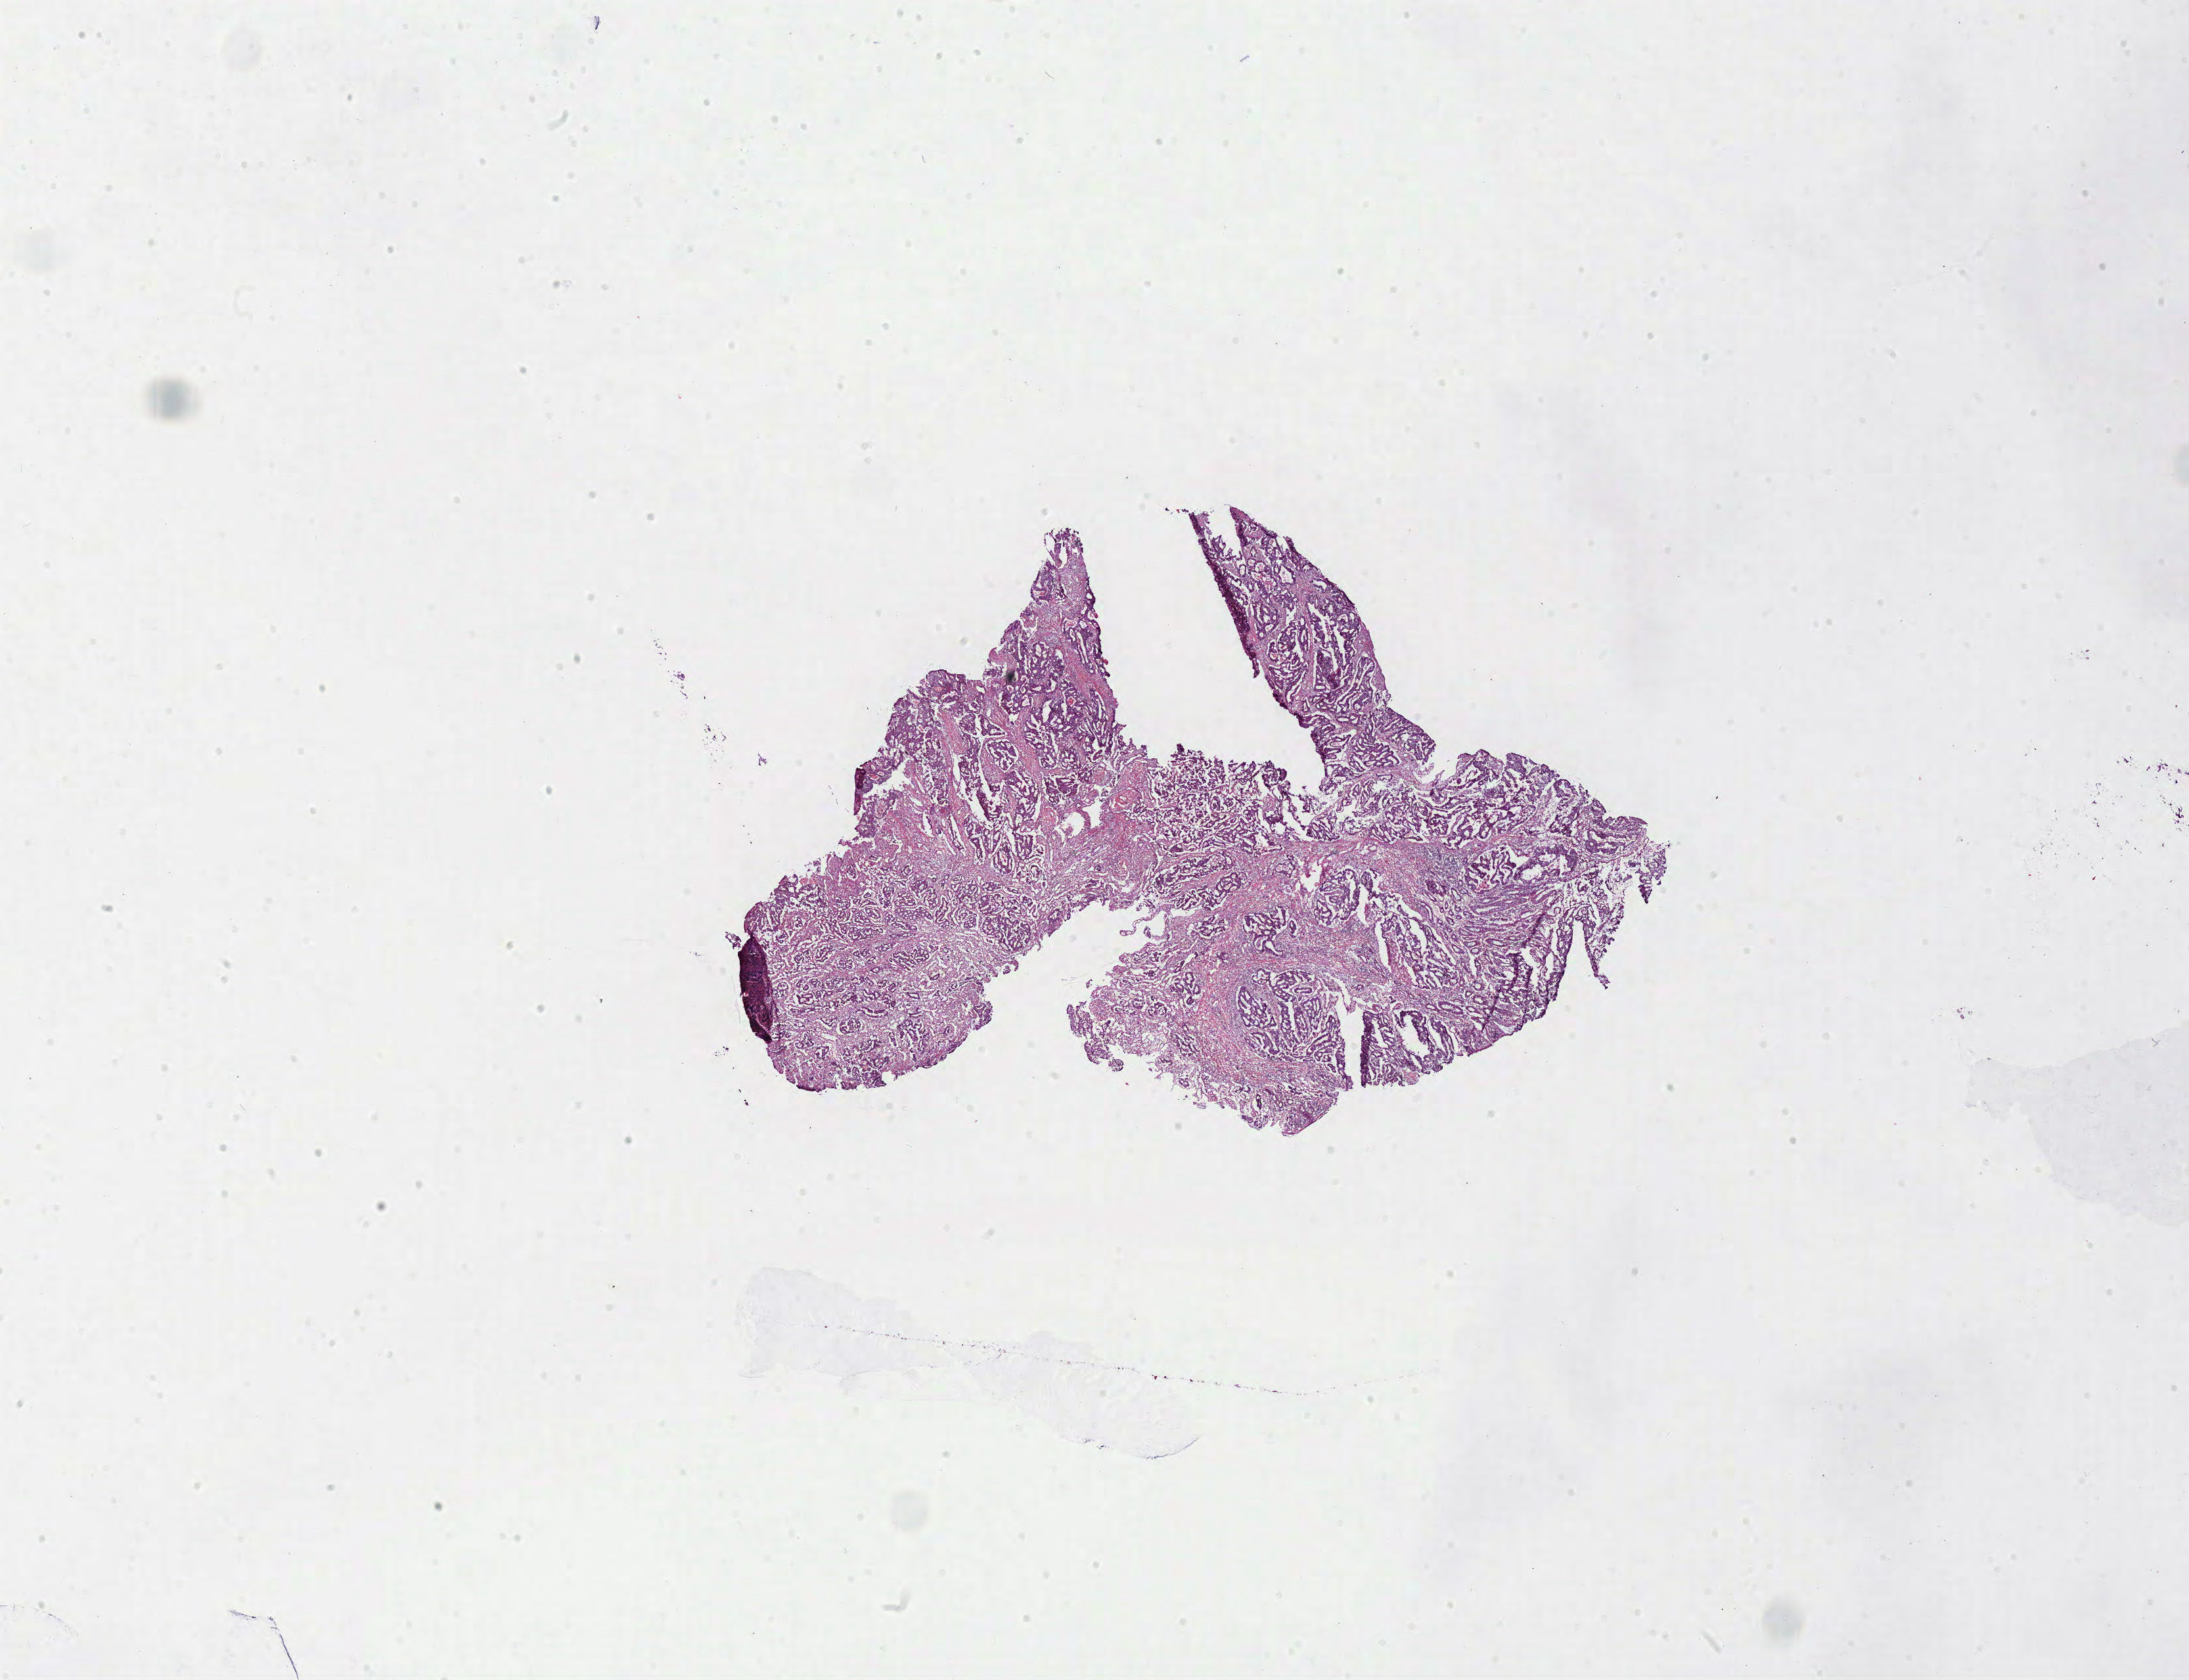
Digitized H&E-stained tissue section (whole slide), low-resolution overview of the scanned area, about 26.3 x 20.1 mm. Frozen section from the bottom of the tissue portion. Rectum, primary tumour sample. Patient: male, age at initial diagnosis 48 years. Slide review estimates, as recorded: tumour cells 77%, tumour nuclei 80%, normal cells 3%, stromal cells 15%, necrosis 5%.
- histologic diagnosis: Adenocarcinoma, NOS (rectosigmoid junction)
- AJCC pathologic stage: I (6th edition)